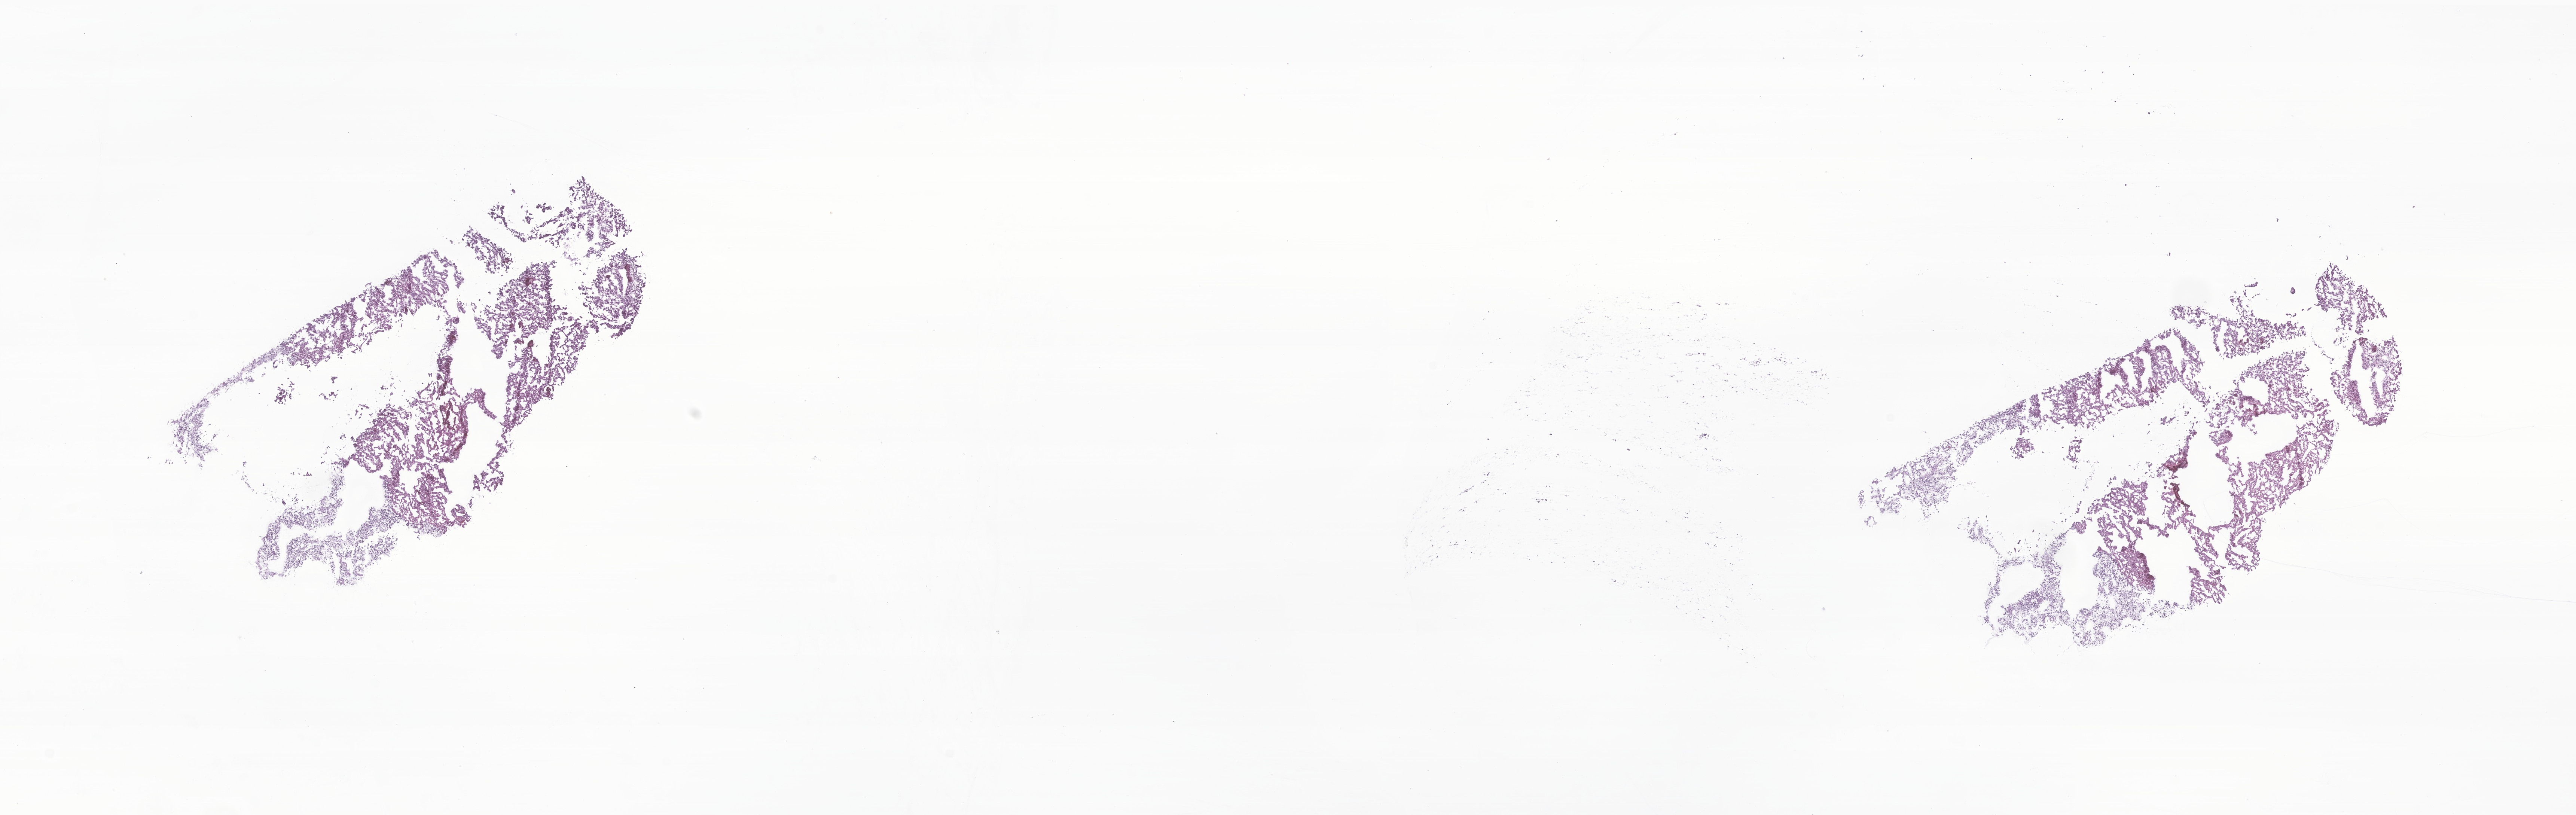
Digitized hematoxylin and eosin (H&E)-stained section of tumor tissue from the brain — low-resolution overview of the scanned area, about 29.0 x 9.2 mm. Frozen section. Patient: female, age 127 months (10 years 7 months).
Diagnosis (ICD-O-3 morphology term): Oligodendroglioma, NOS.